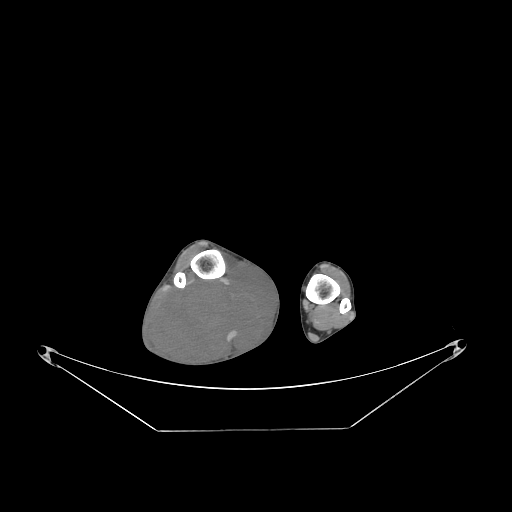
CT of an extremity soft-tissue mass (from a PET/CT study), one axial slice. Position 58 of 267 along the scan axis. Soft-tissue window (W 400 / L 40 HU). 3.75 mm slice thickness. 512 × 512 image matrix, field of view 500 × 500 mm. Male patient. From the clinical record (not read from this slice): histological type: liposarcoma - round cell; grade: high; site of the primary tumour: right calf.
Structures marked on this image (expert contour drawn on MRI and transferred to this co-registered scan by the dataset authors):
- gross tumour volume (mass): bounding box [x1, y1, x2, y2] px = [153, 267, 277, 366]